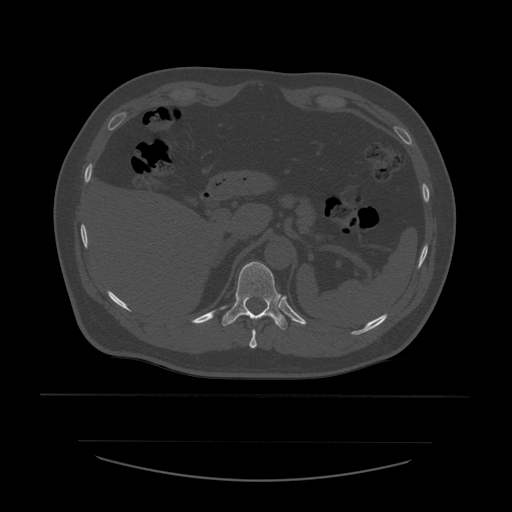
CT including the spine, one axial slice; position 279 of 532 along the scan axis; reconstruction kernel STANDARD; bone window (W 1800 / L 400 HU); 1.25 mm slice thickness; 512 × 512 image matrix. Patient age 44 years. From the clinical record (not read from this slice): primary cancer: soft tissue sarcoma.
Annotated regions visible in this slice (semi-automatic segmentation, software-assisted and operator-edited):
- T10 vertebra: bounding box (x1, y1, x2, y2) in pixels: (249, 329, 257, 349)
- T11 vertebra: (222, 262, 287, 331)